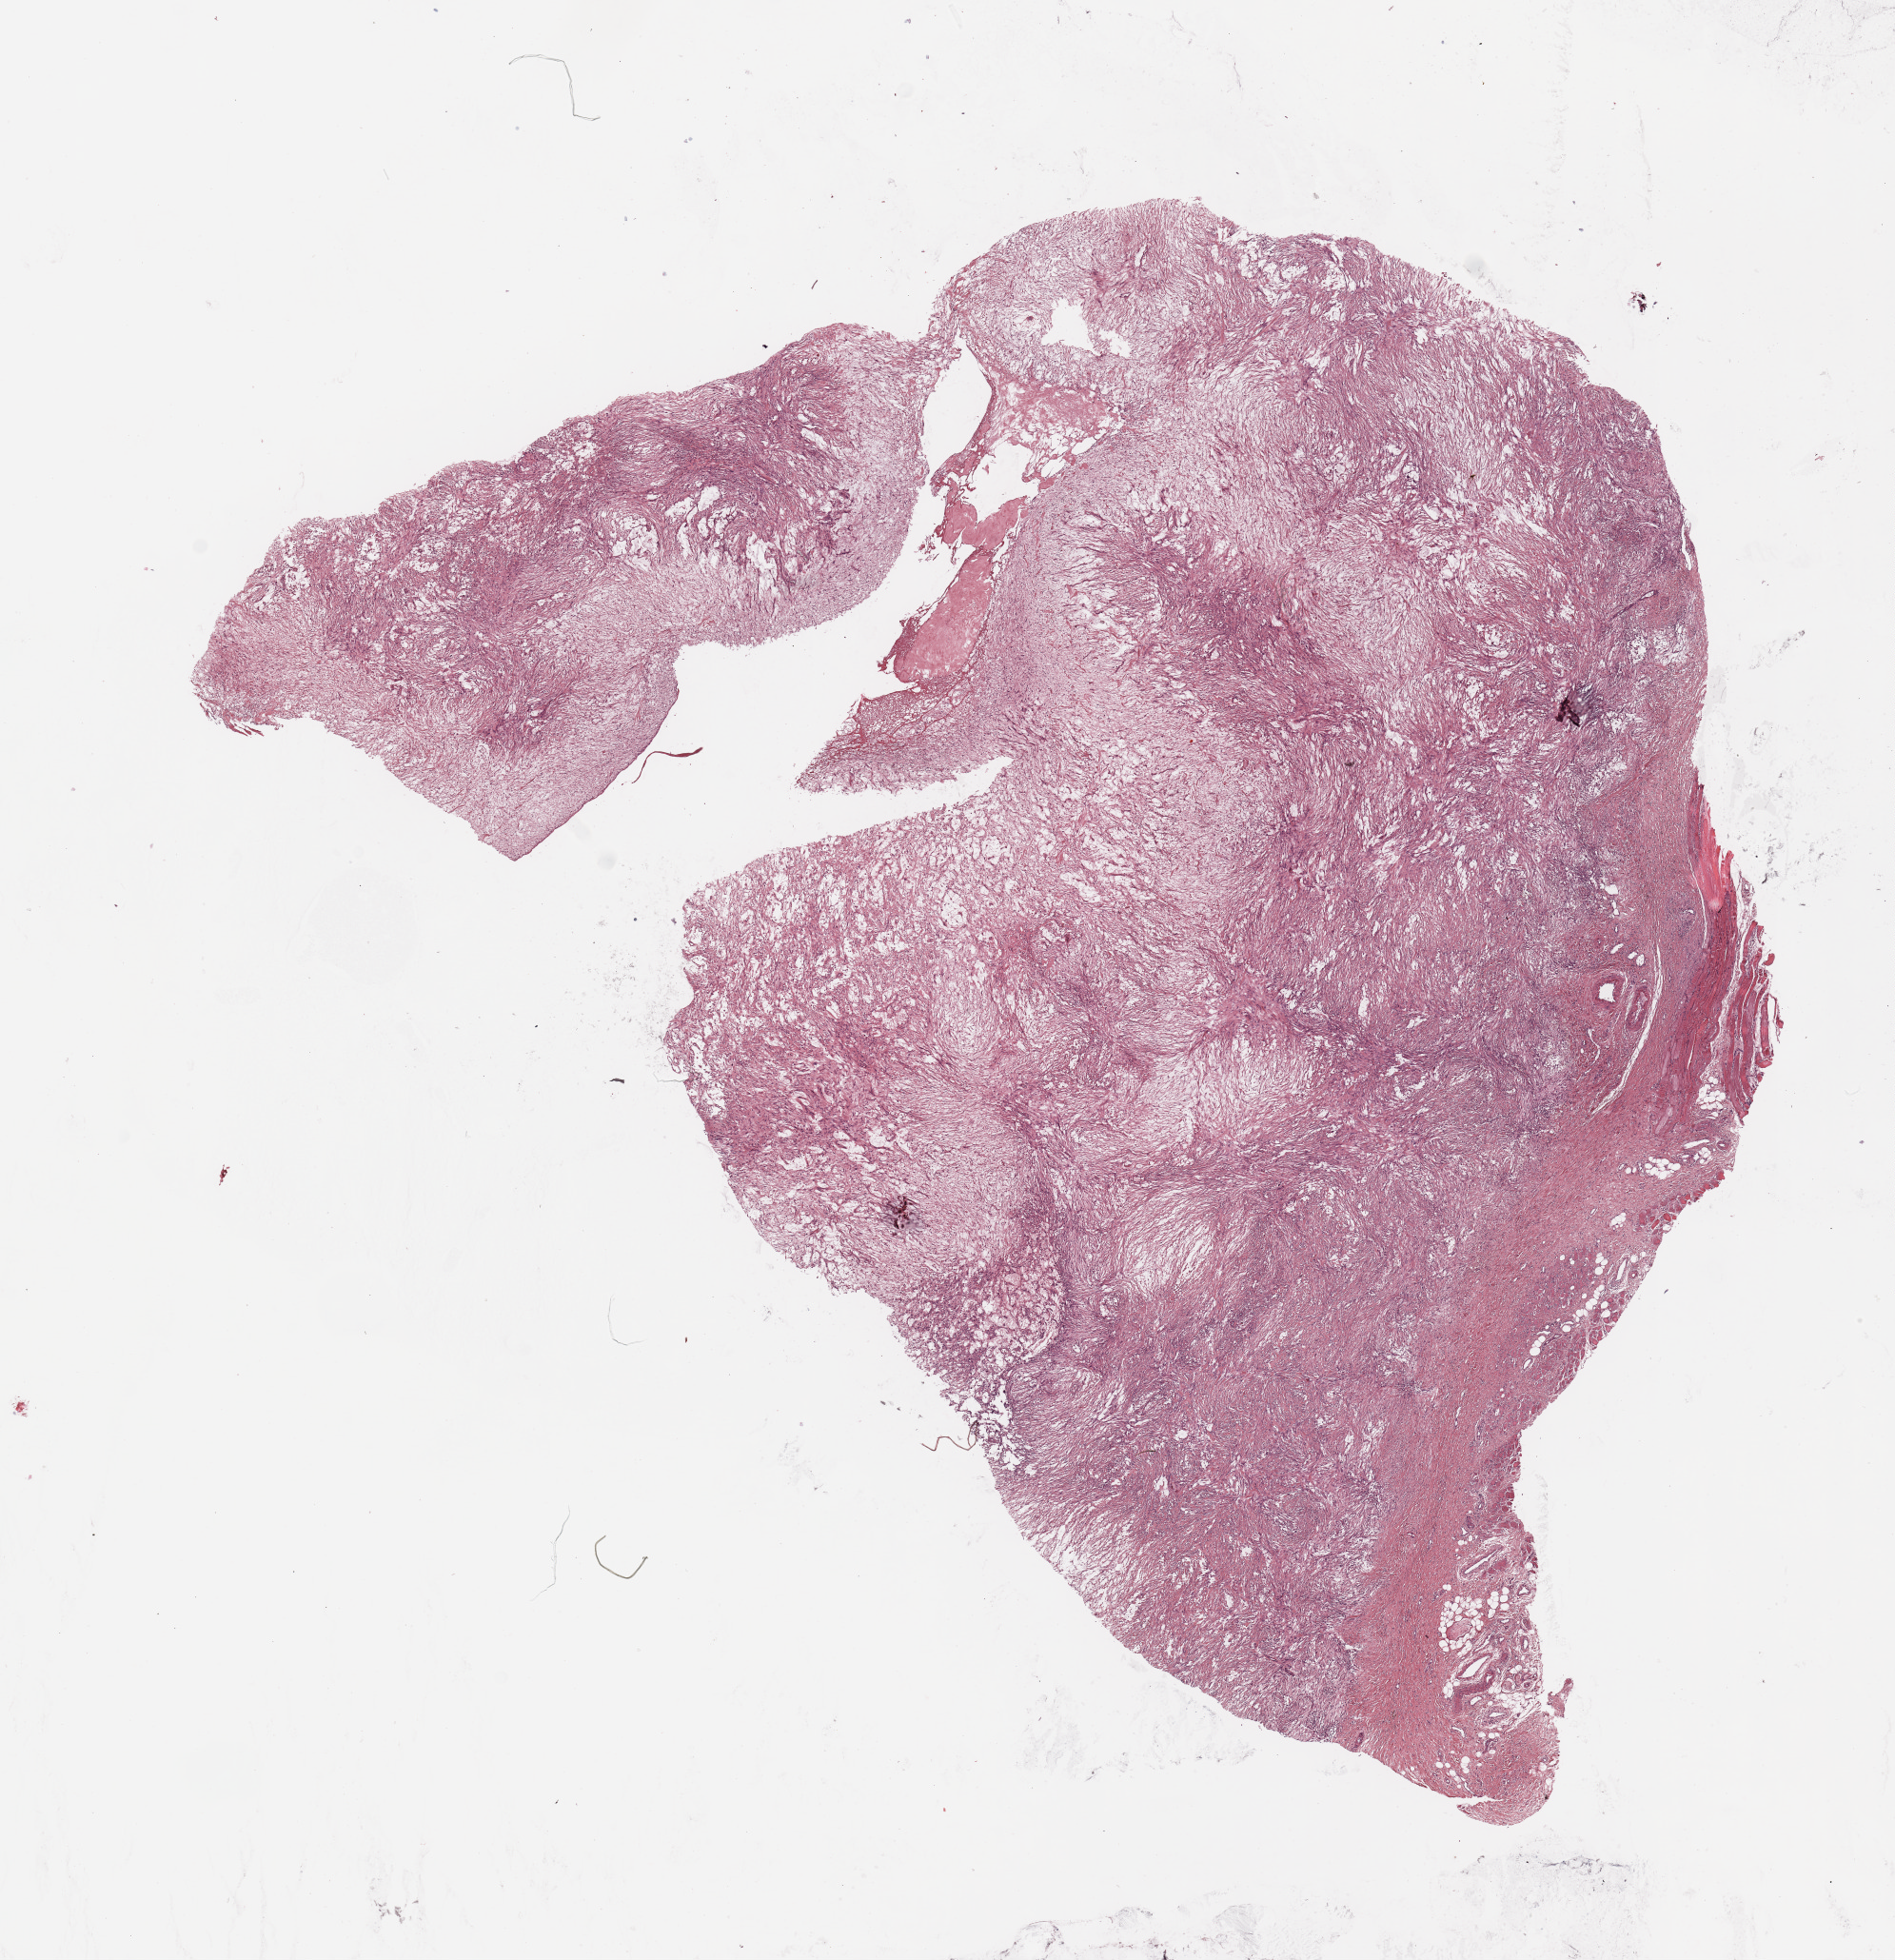
H&E-stained whole-slide image, low-resolution overview of the scanned area, about 15.8 x 16.3 mm (acquisition: 20x scan). Tumour tissue sample. Patient: female, age 67 years.
- patient diagnosis (cohort enrolment): sarcoma (site not recorded at cohort level)
- primary tumour site (as recorded): superficial trunk